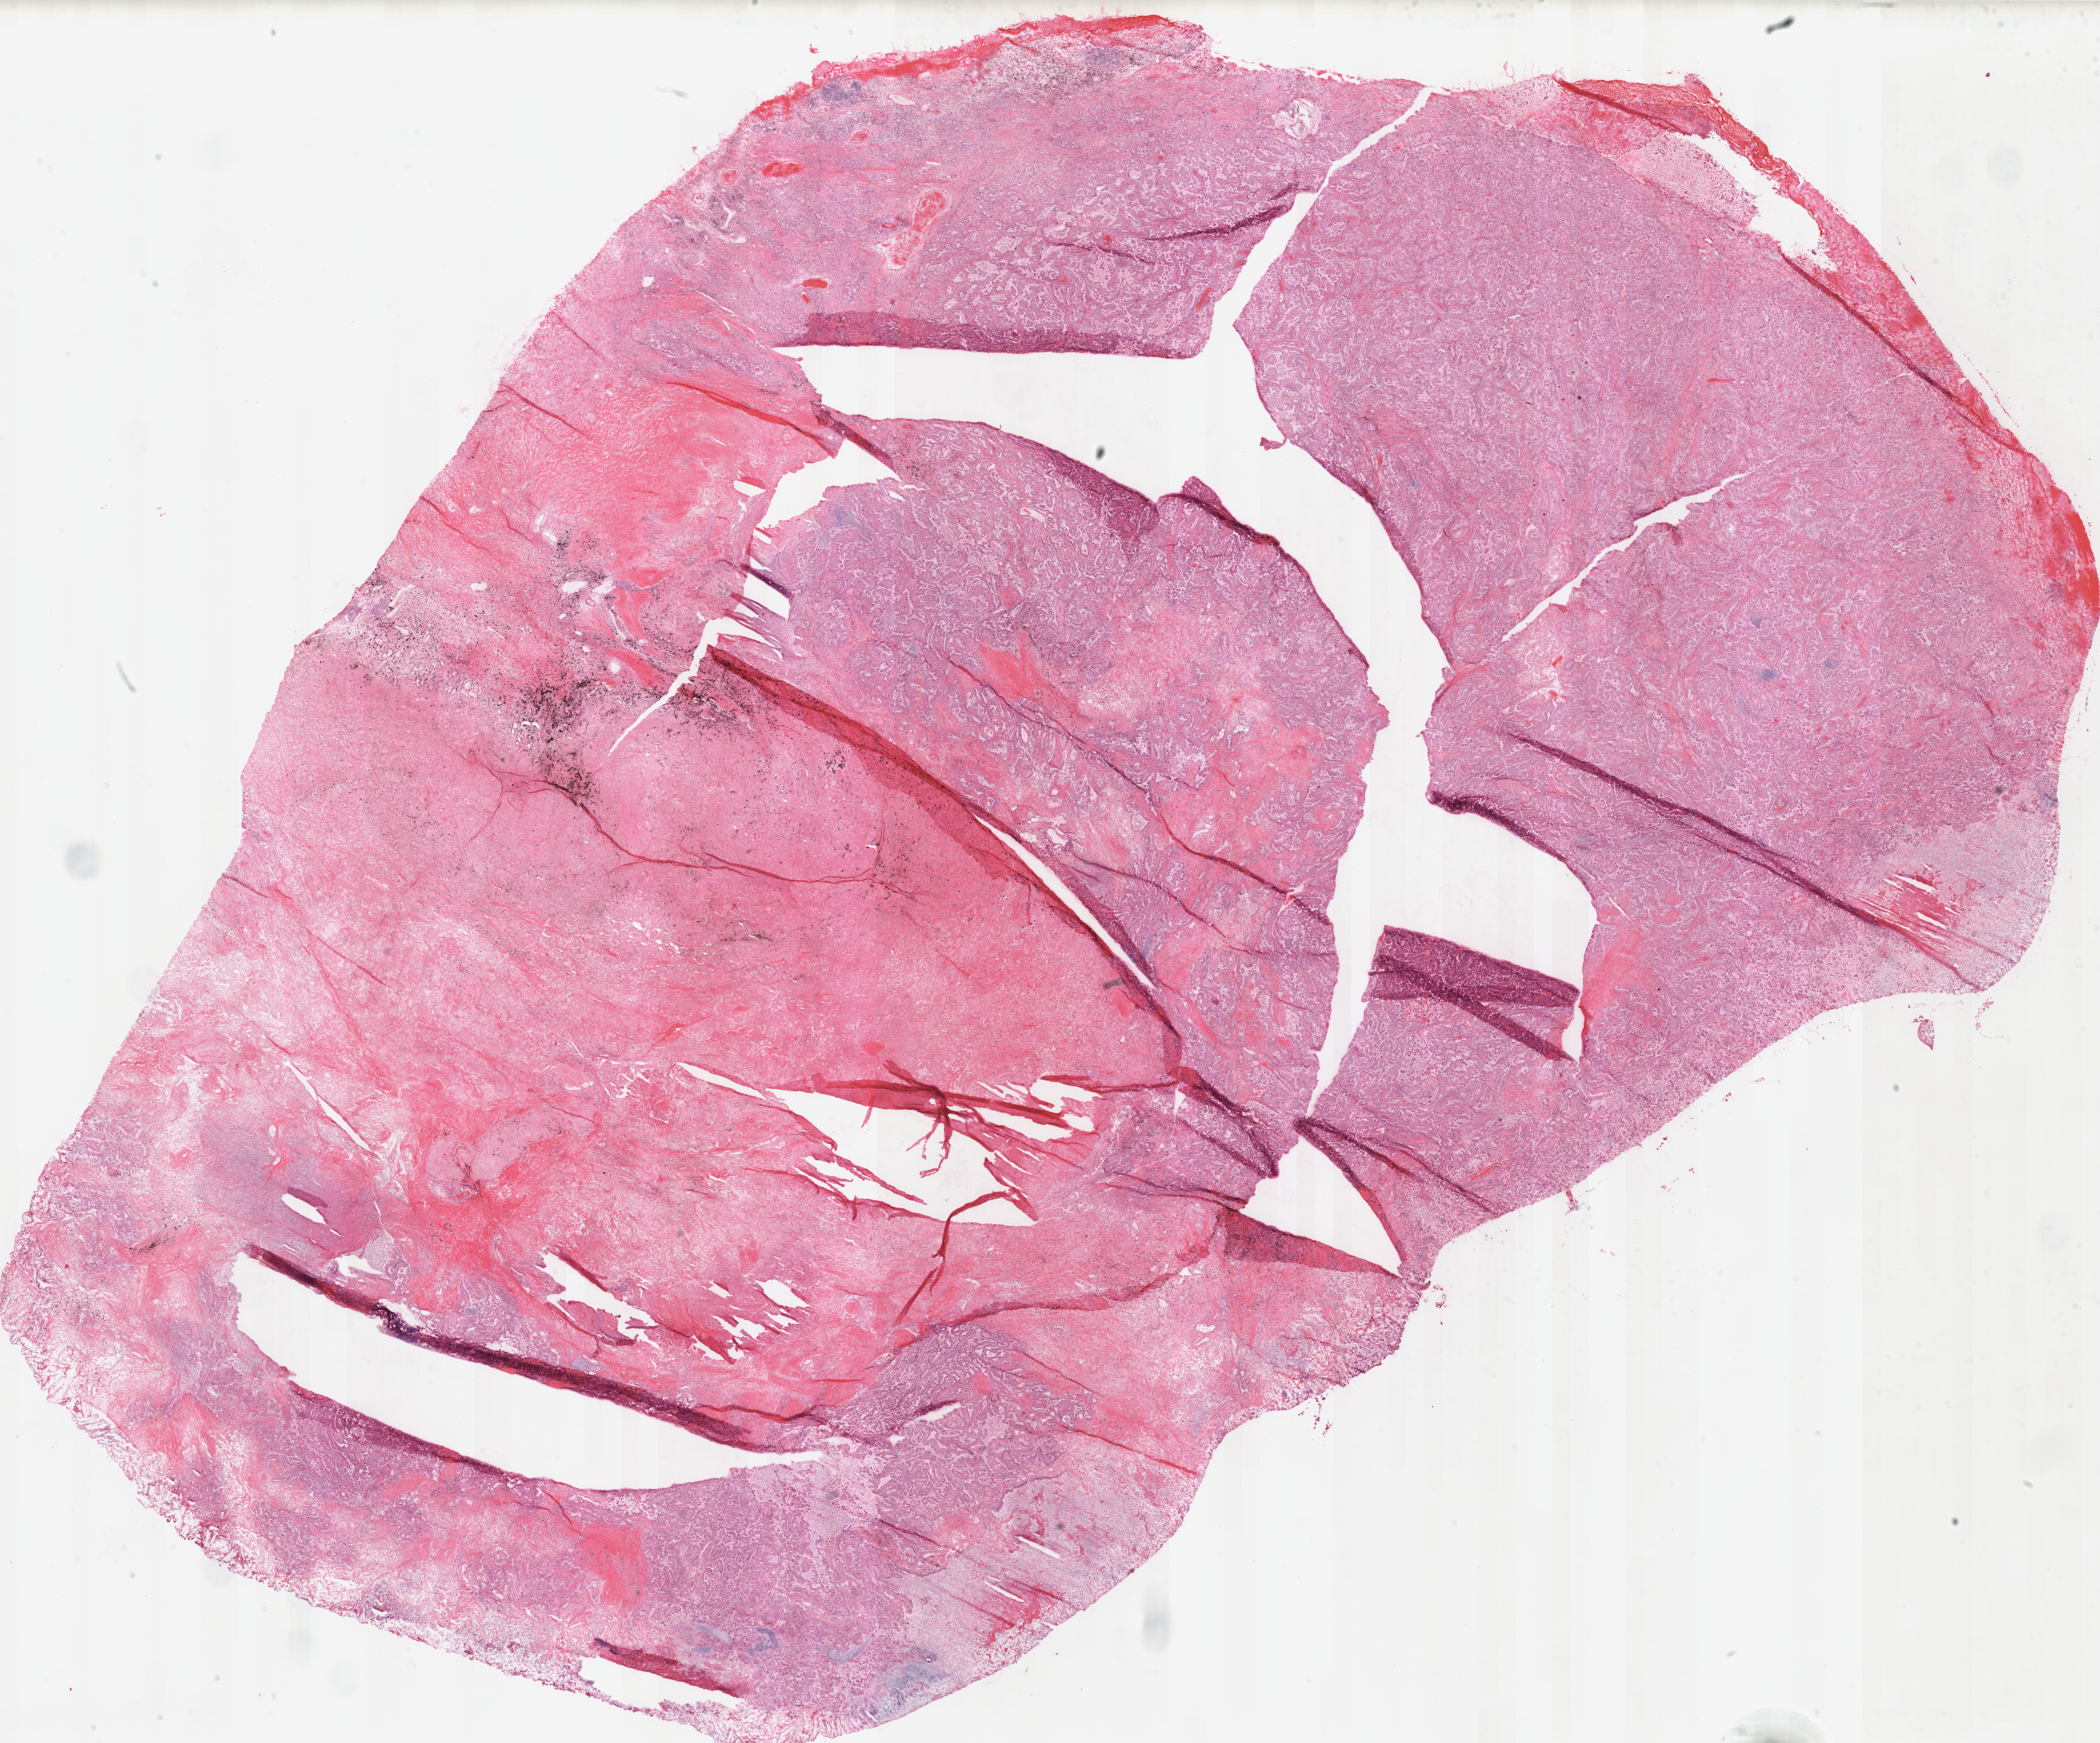
Digitized Hematoxylin and eosin (H&E) stained tissue section (whole slide), low-resolution overview of the scanned area, about 27.0 x 22.4 mm (acquisition: 40x scan). Frozen section from the top of the tissue portion. Lung, primary tumour sample. Male patient; age at initial diagnosis 61 years. Pathologist review of this section (percent, as recorded): tumour cells 60%, tumour nuclei 65%, stromal cells 30%, necrosis 10%. Infiltration values recorded for this section: lymphocyte infiltration 20%, monocyte infiltration 0%, neutrophil infiltration 0%.
- AJCC pathologic stage: IB (7th edition)
- diagnosis: Bronchiolo-alveolar carcinoma, non-mucinous (upper lobe, lung)
- laterality: left